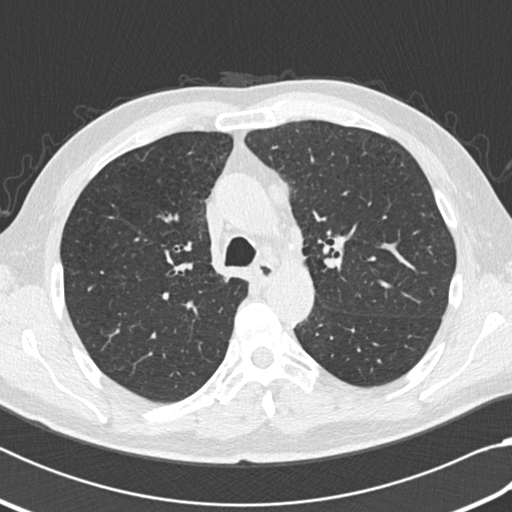
Axial slice from a low-dose chest CT screening exam; third screening round (two years after baseline); lung window (W 1500 / L -600 HU); standard (soft-tissue) reconstruction kernel (B30f); slice 63 of 207 in the series; 512 × 512 image matrix. Male, age 64 years at enrolment. Current smoker at enrolment.
Expert reader's lesion annotation, bounding box (x1, y1, x2, y2) in pixels: (252, 177, 288, 213). No non-calcified nodule or mass ≥4 mm was recorded by the screening reader at this exam. Official screen result: negative screen, significant abnormalities not suspicious for lung cancer. Lung cancer was diagnosed 163 days after this screen: small cell carcinoma, NOS, mediastinum, stage IV (AJCC 6th edition).